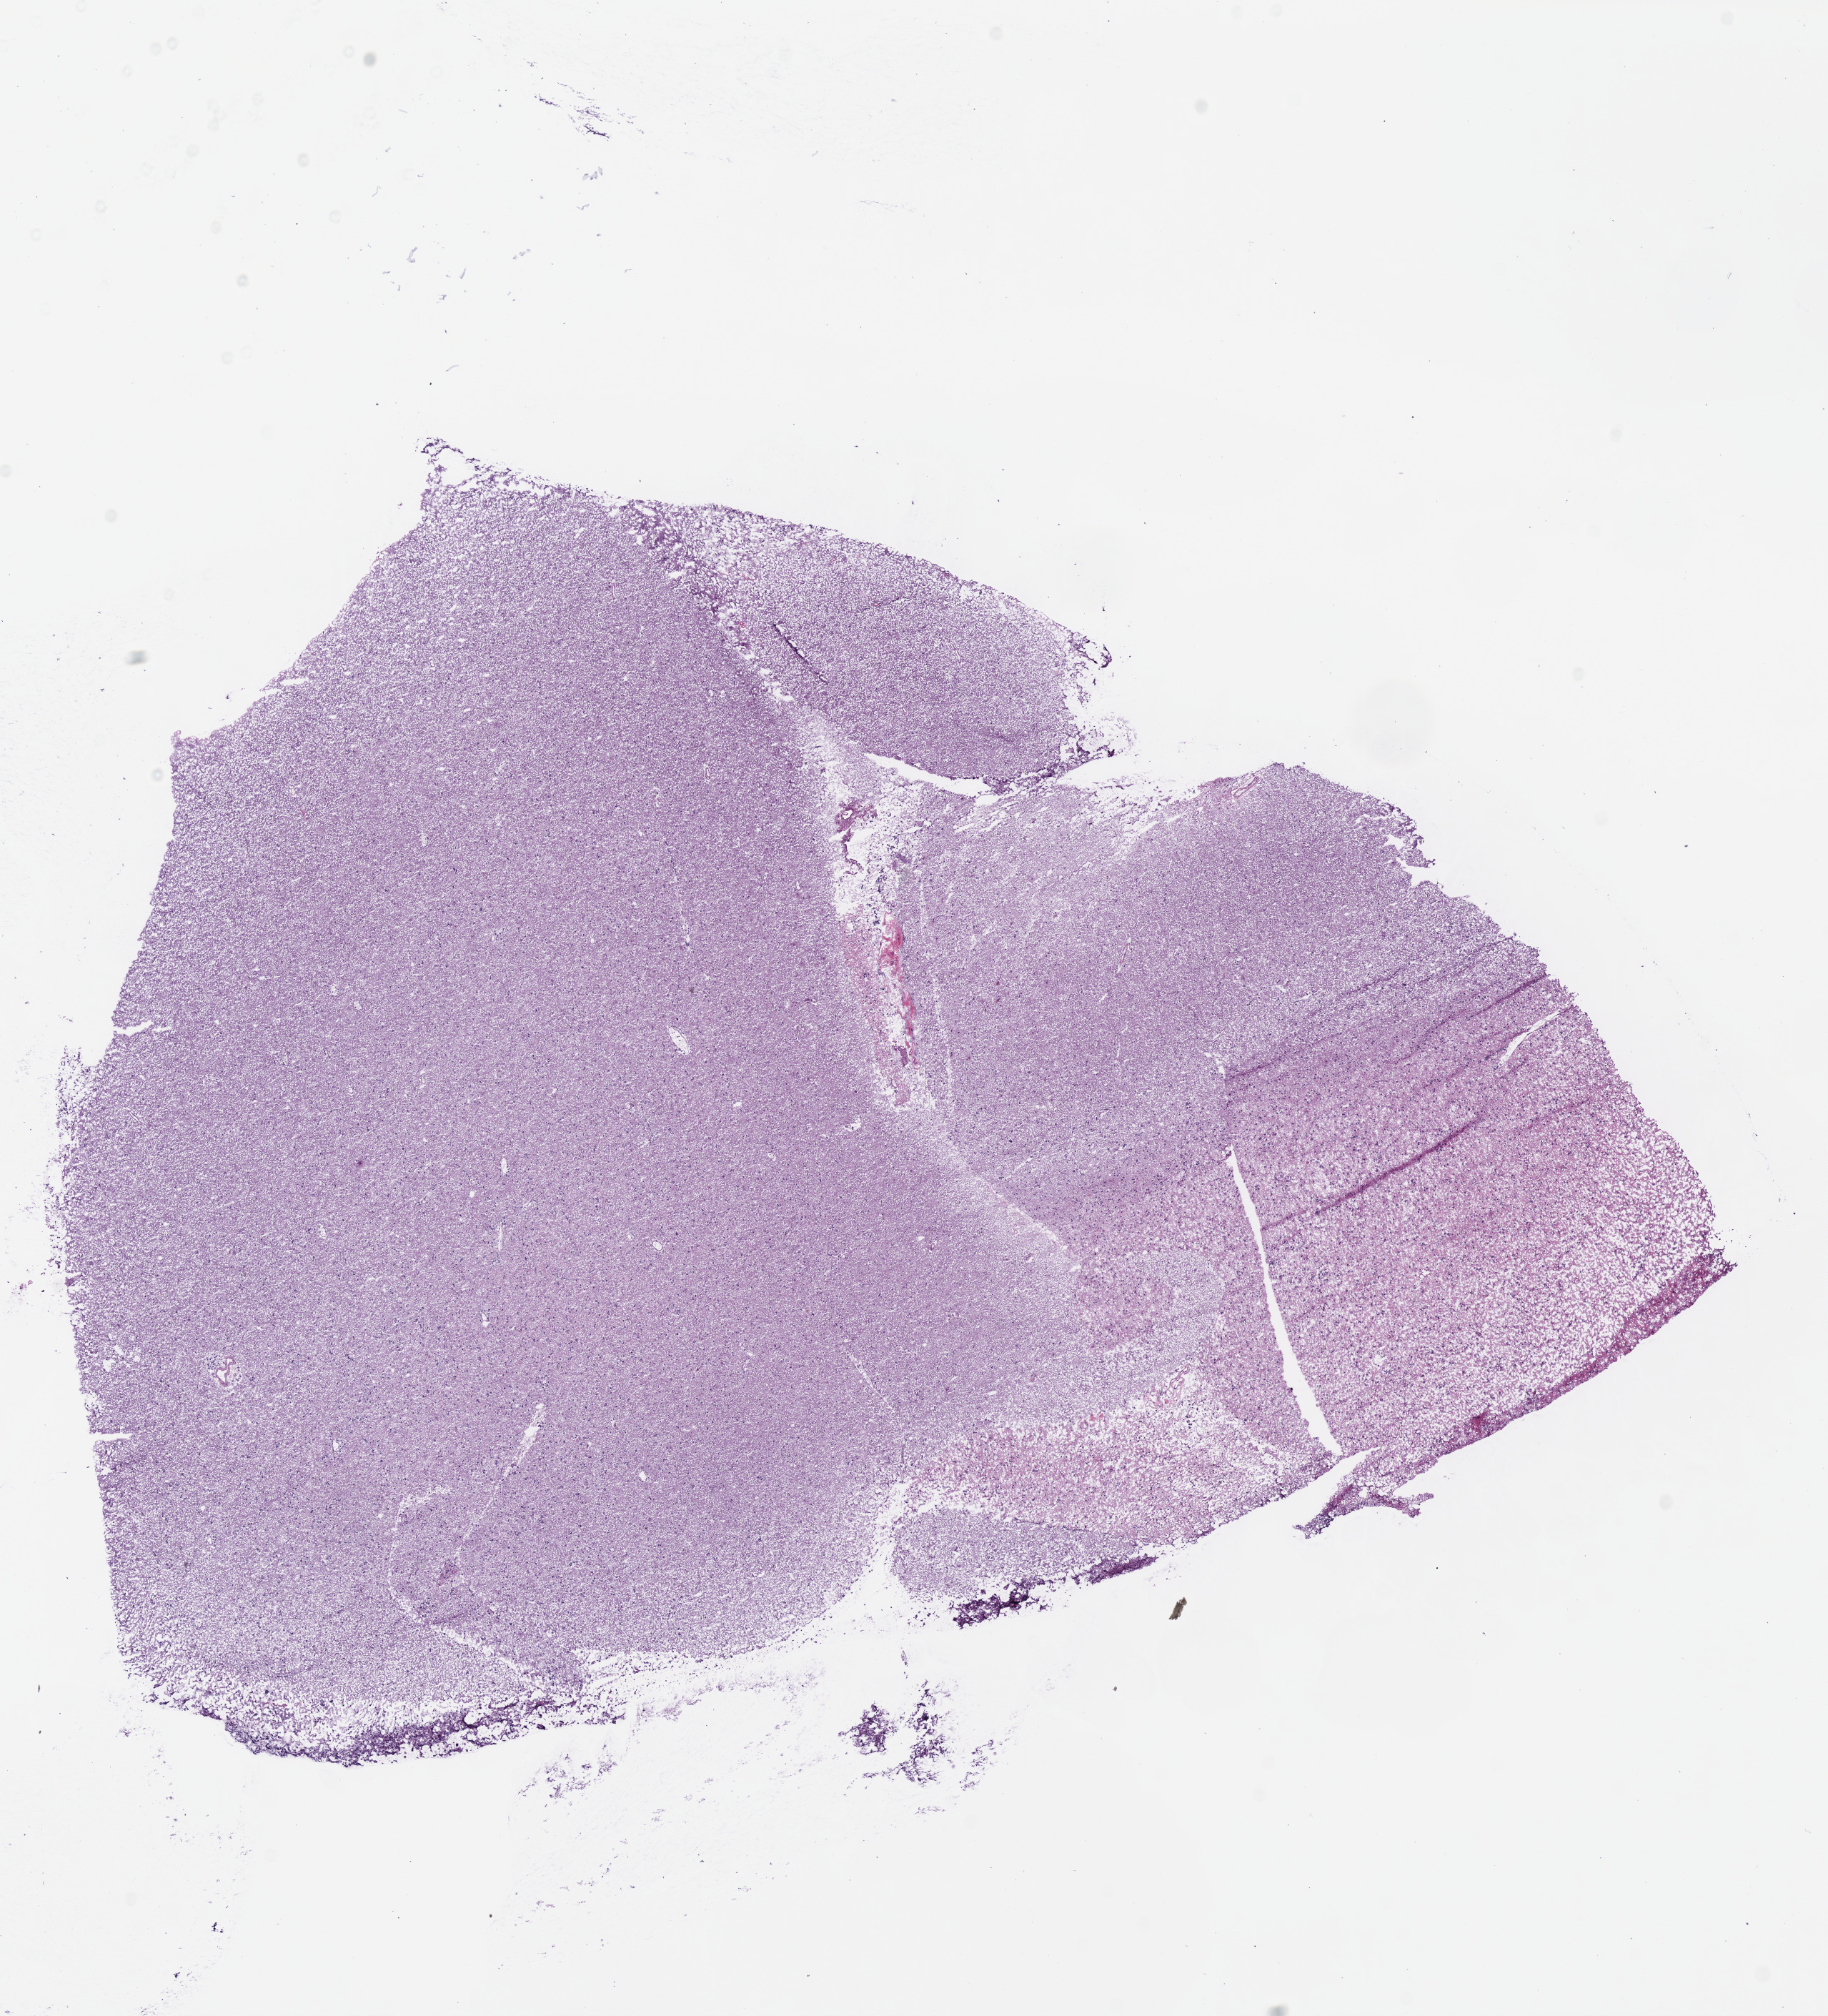
Digitized H&E-stained tissue section (whole slide), a low-resolution overview of the entire scanned area, about 10.1 x 11.1 mm (acquisition: 40x scan); frozen section from the bottom of the tissue portion; primary tumour sample from the brain. Patient: male, age at initial diagnosis 59 years. Histologic grade: G3 (poorly differentiated). Pathologist review of this section (percent, as recorded): tumour cells 100%, tumour nuclei 65%, normal cells 0%, stromal cells 0%, necrosis 0%.
* diagnosis: Oligodendroglioma, anaplastic
* laterality: left